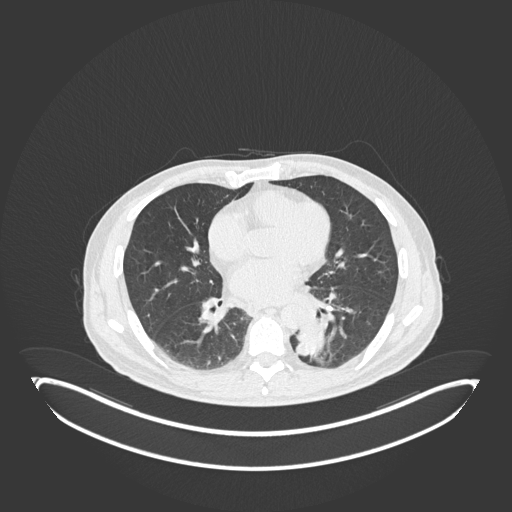
Chest CT, one axial slice; position 78 of 251 along the scan axis; lung window (W 1500 / L -600 HU); 1 mm slice thickness; 512 × 512 image matrix. Male patient, age 72 years. From the clinical record (not read from this slice): clinical TNM (as recorded): T2b N0 M1.
Annotated regions visible in this slice (rectangle marked by the reading radiologist):
- lung tumour (recorded histology: adenocarcinoma): bounding box [x1, y1, x2, y2] px = [290, 317, 330, 360]